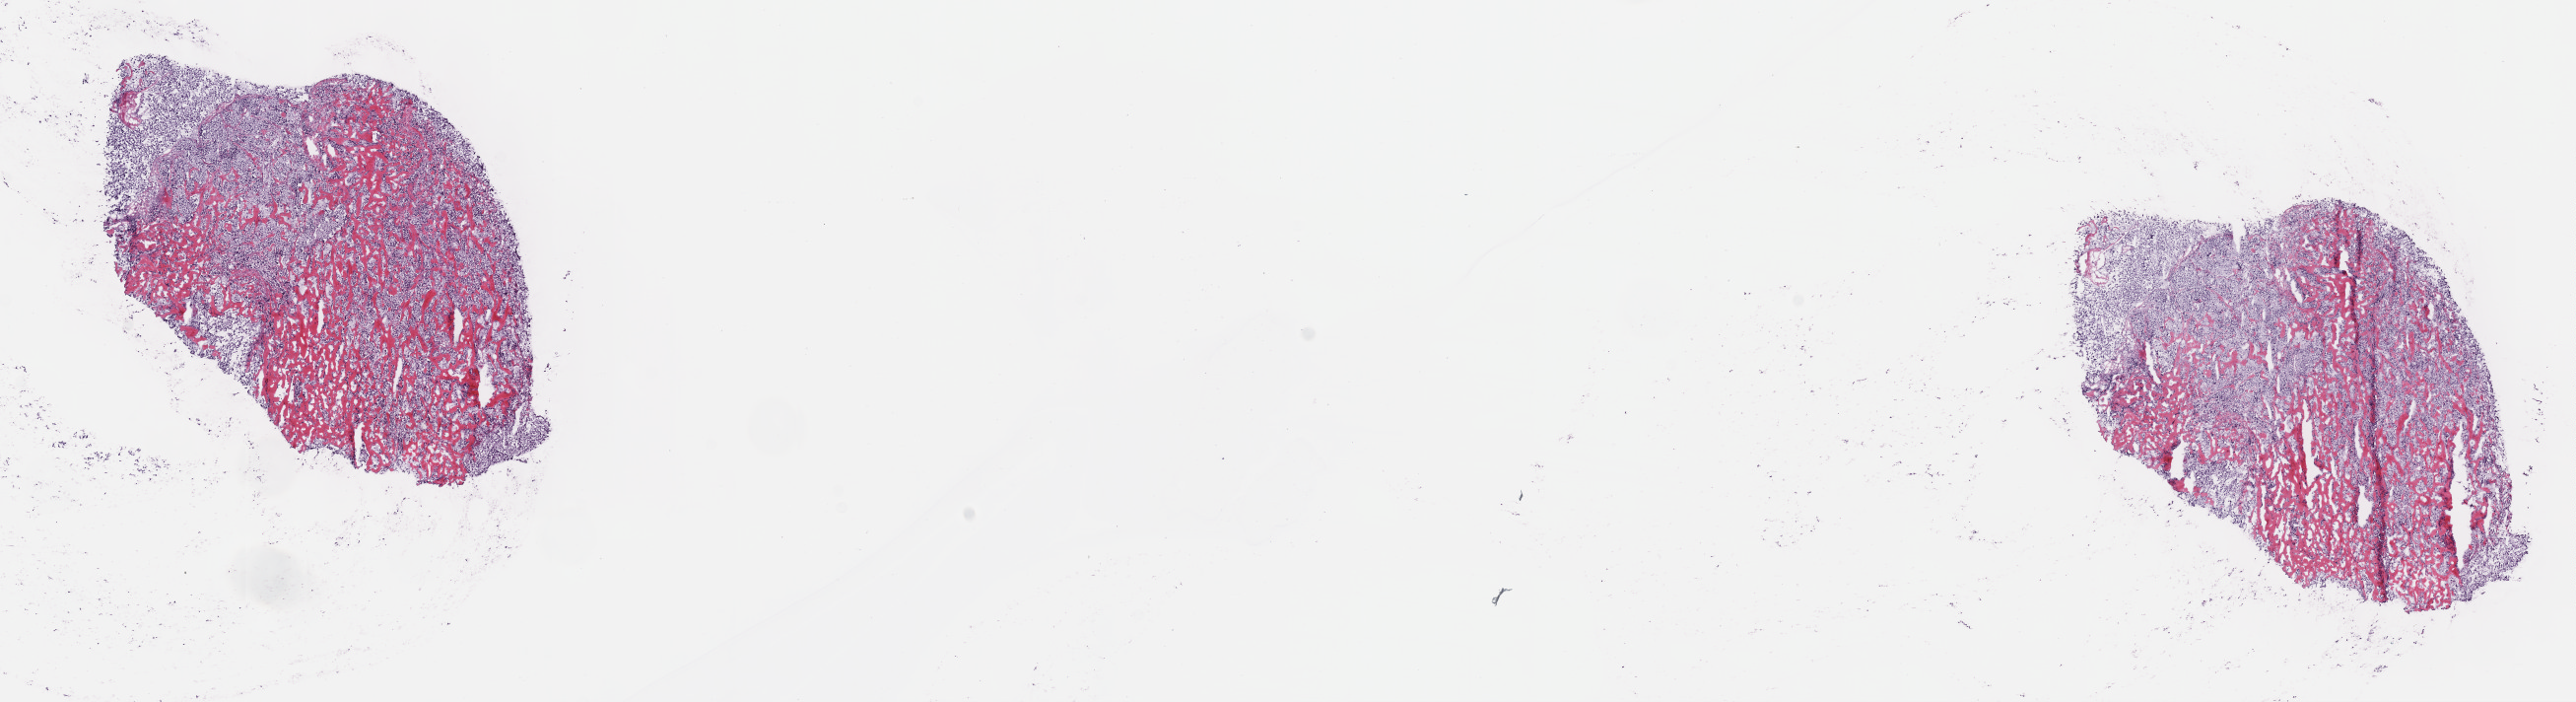
H&E whole-slide image, whole scanned area (about 21.1 x 5.8 mm) shown as a low-resolution overview; frozen section; adrenal gland, primary tumour sample. Female, age 68 years at initial diagnosis.
Histologic diagnosis: Pheochromocytoma, malignant.